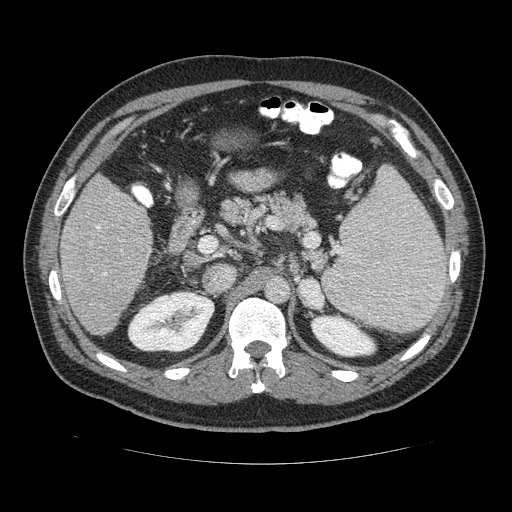
Contrast-enhanced abdominal CT (liver protocol), one axial slice. Slice 69 of 113 in the series (ordered by position). 120 kVp. Soft-tissue window (W 400 / L 40 HU). 2.5 mm slice thickness. 512 × 512 image matrix, field of view 400 × 400 mm. From the clinical record (not read from this slice): diagnosis: hepatocellular carcinoma (patient treated with transarterial chemoembolisation; whether this scan precedes or follows treatment is not stated here); TNM stage (as recorded): Stage-II; Child-Pugh class: B; tumour differentiation: moderately differentiated; tumour nodularity: multinodular.
Structures marked on this image (semi-automatically segmented with operator editing):
- liver parenchyma outside the tumour (the mass and vessels are separate outlines, so this box may not span the whole liver): bounding box <58,172,154,338> (left, top, right, bottom; pixels)
- liver vessels: <97,220,151,276>